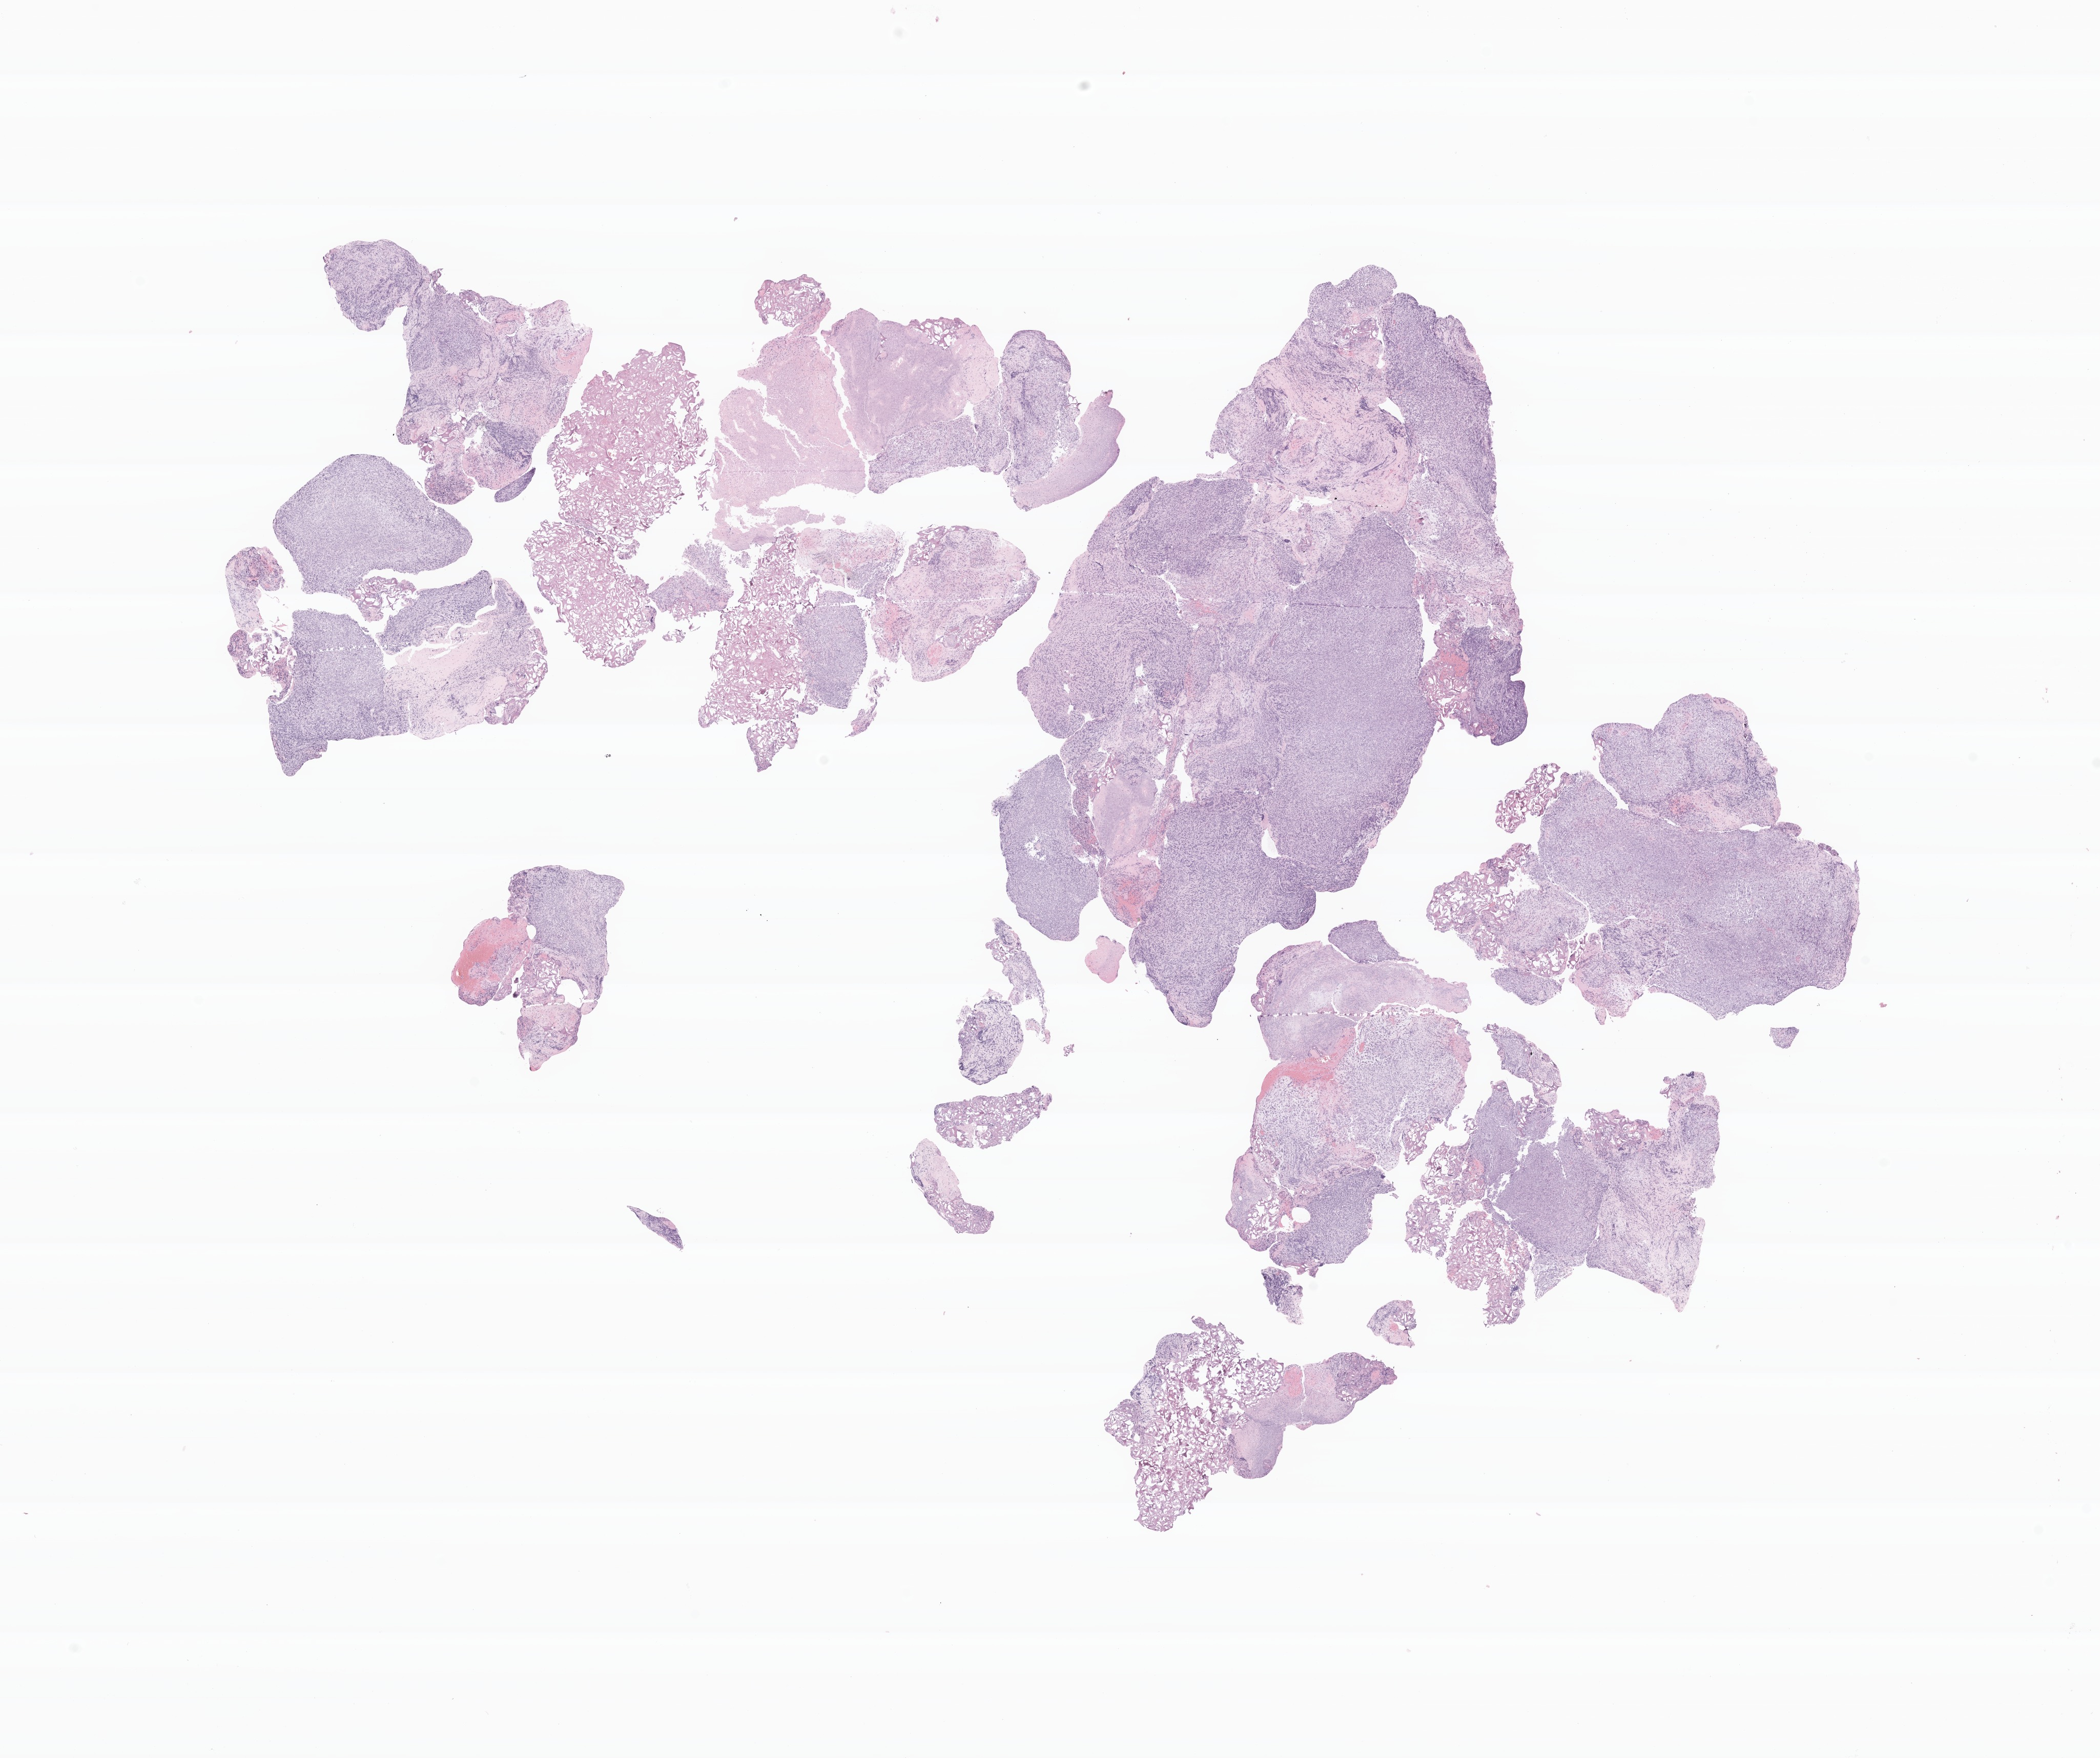
Digitized hematoxylin and eosin (H&E)-stained section of tumor tissue from the spinal cord — low-resolution overview of the scanned area, about 17.2 x 14.4 mm; formalin-fixed paraffin-embedded section. Patient female; age 49 months.
• diagnosis (ICD-O-3 morphology term): Neoplasm, malignant